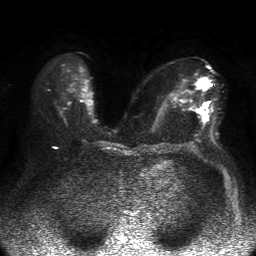
Breast MRI, one axial slice; position 23 of 50 along the scan axis; diffusion-weighted series; image 2 of 4 stored at this slice position (different b-values; order by instance number); 1.5 T; 4 mm slice thickness; 256 × 256 image matrix, field of view 360 × 360 mm. Female patient.
Structures marked on this image (expert manual segmentation):
- tumour on diffusion-weighted imaging: bounding box [x1, y1, x2, y2] px = [199, 77, 209, 117]